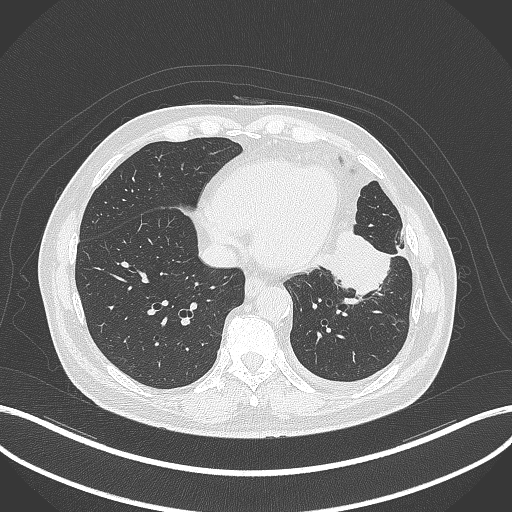
Chest CT, one axial slice. Lung window (W 1500 / L -600 HU). 1 mm slice thickness. 512 × 512 image matrix. Male patient, age 68 years. From the clinical record (not read from this slice): clinical TNM (as recorded): T2b N0 M0.
Outlined on this slice (bounding box drawn by a radiologist):
- lung tumour (recorded histology: squamous cell carcinoma): bounding box [x1, y1, x2, y2] px = [319, 228, 394, 300]